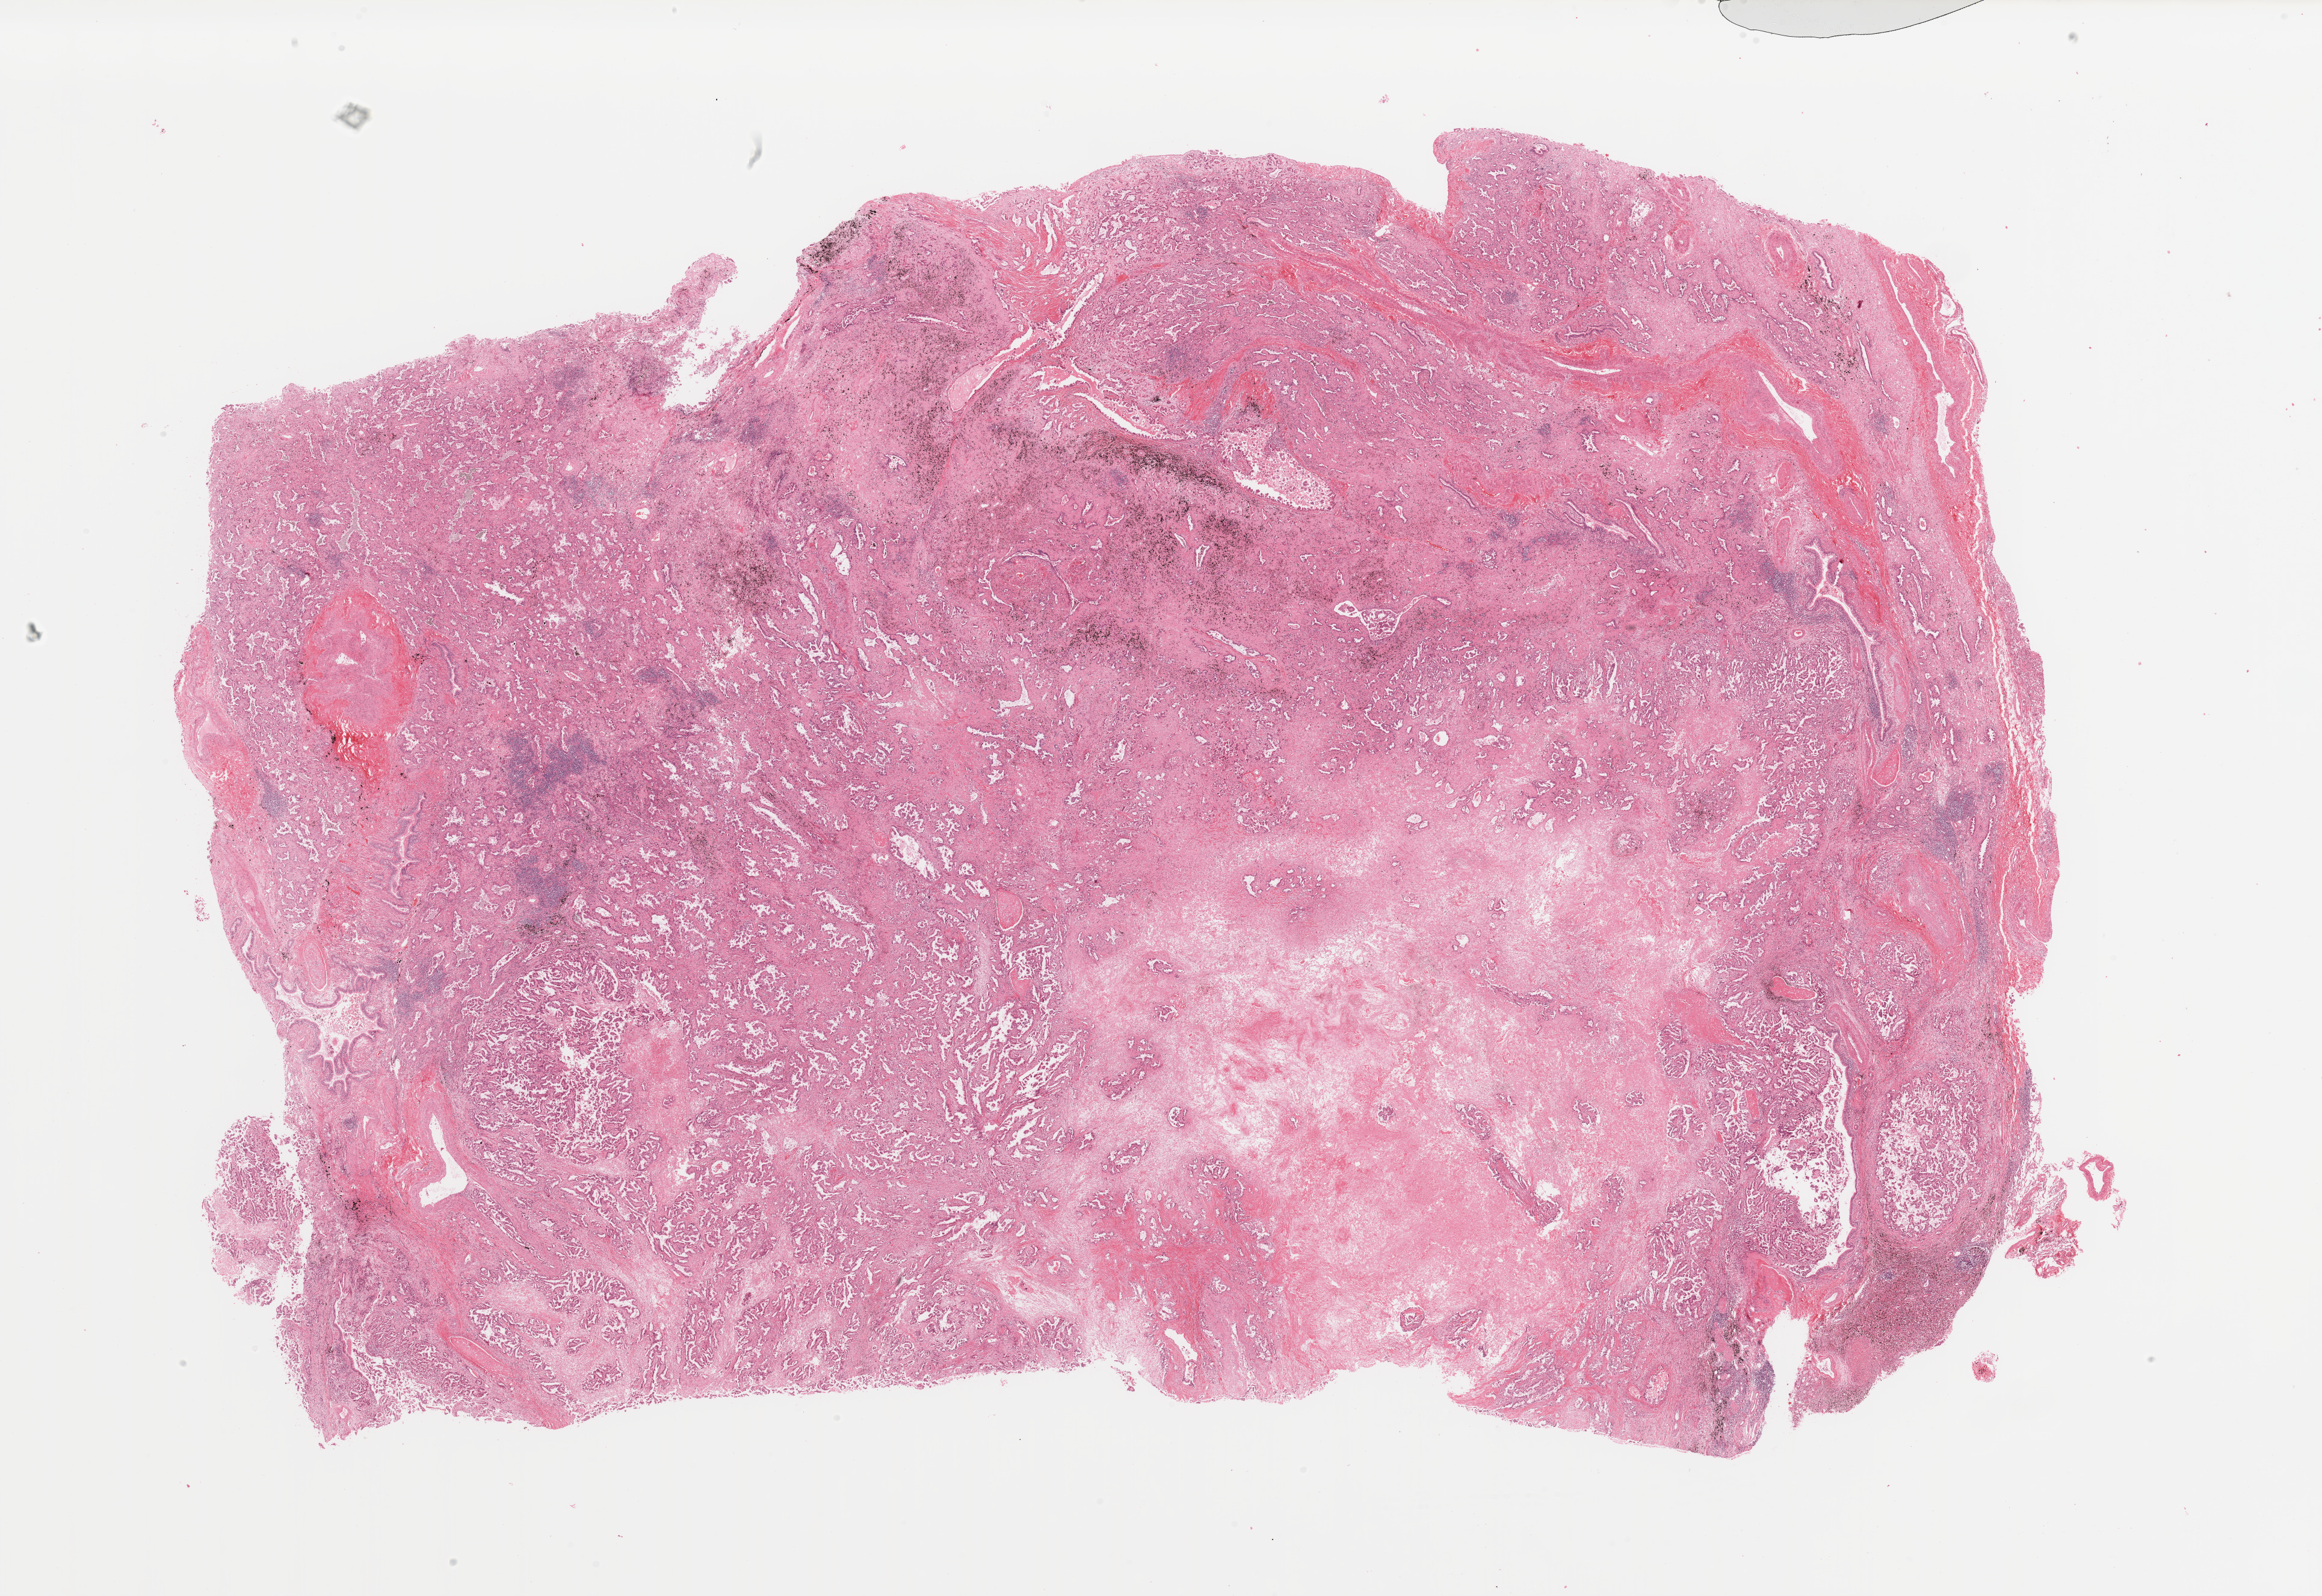
Whole-slide histology image, H&E, whole scanned area (about 30.5 x 21.0 mm, acquisition: 20x scan) shown as a low-resolution overview; tumour tissue sample, lung. 69-year-old female patient. Histologic grade: G2 (moderately differentiated).
Histologic diagnosis: Adenocarcinoma, NOS. AJCC pathologic stage: IIIA.